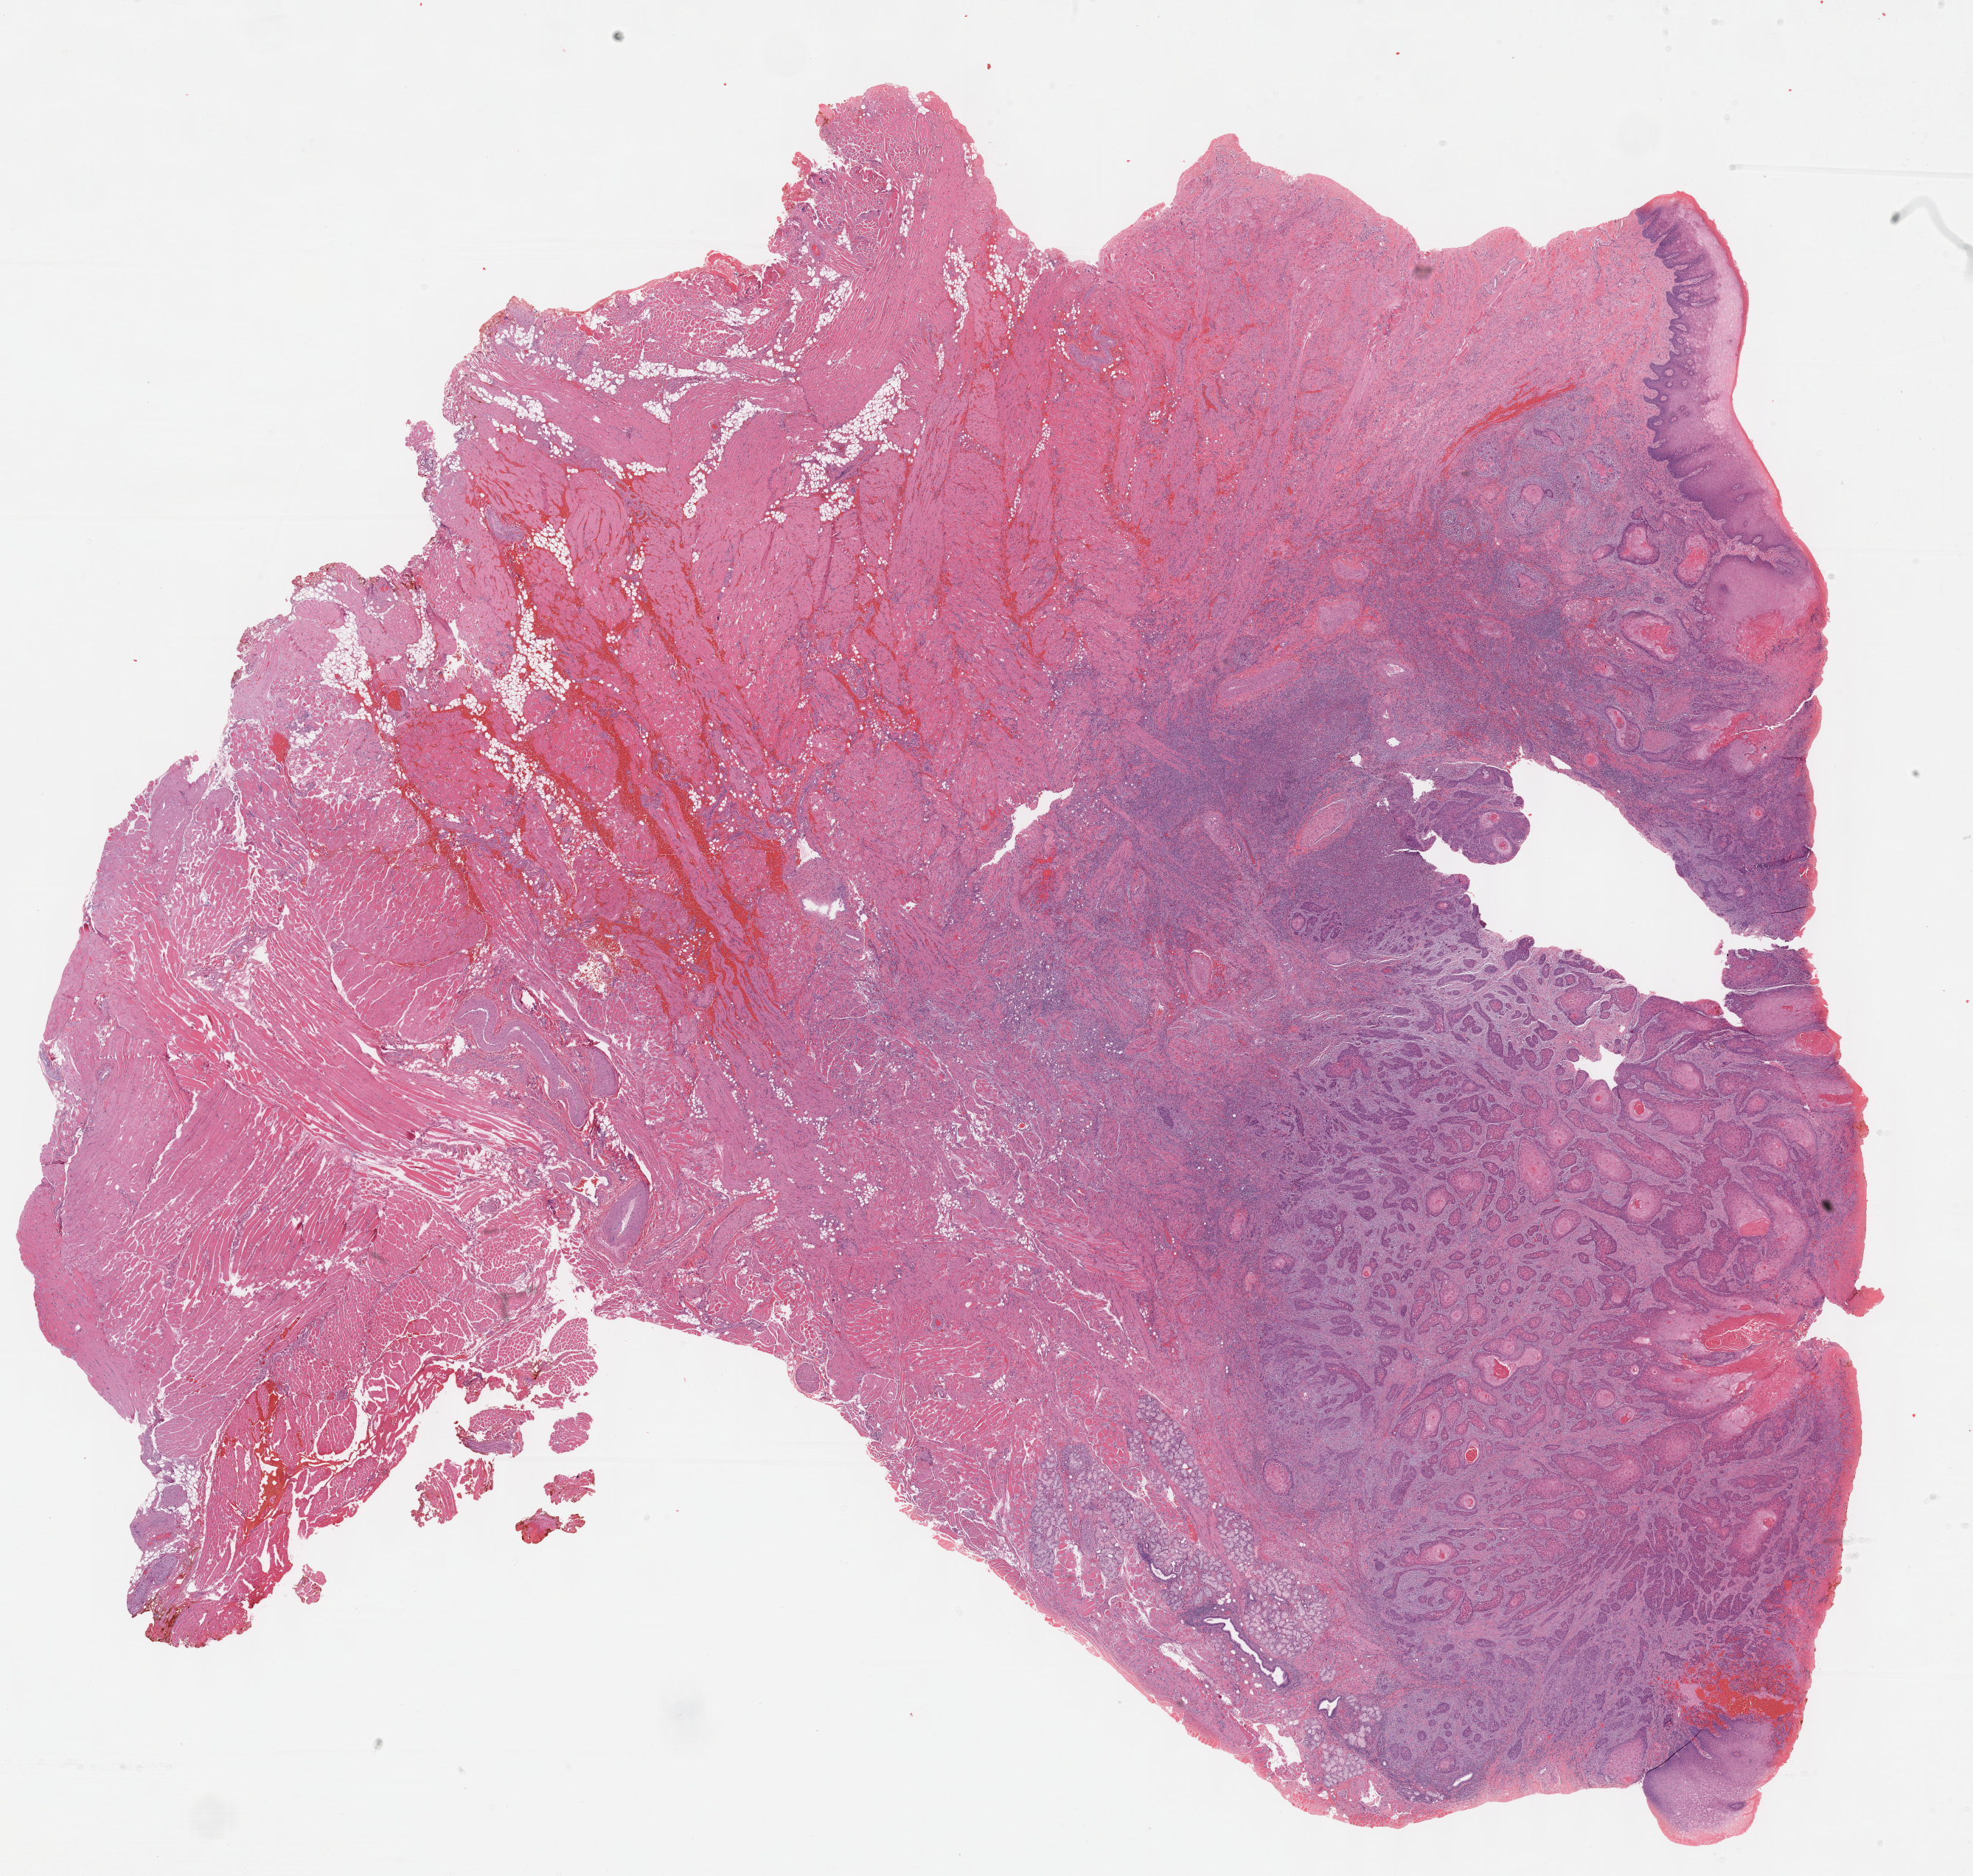
Whole-slide histology image, Hematoxylin and eosin (H&E) stained — whole scanned area (about 21.6 x 20.6 mm, from a 40x scan) shown as a low-resolution overview. Formalin-fixed paraffin-embedded (FFPE) diagnostic section. Sample: primary tumour, head and neck. Patient: male, age at initial diagnosis 50 years. Histologic grade: G2 (moderately differentiated).
Laterality: right. Histologic diagnosis: Squamous cell carcinoma, NOS (tongue, NOS). Lymph nodes positive (case pathology): 1 of 26 examined. AJCC pathologic stage: III.